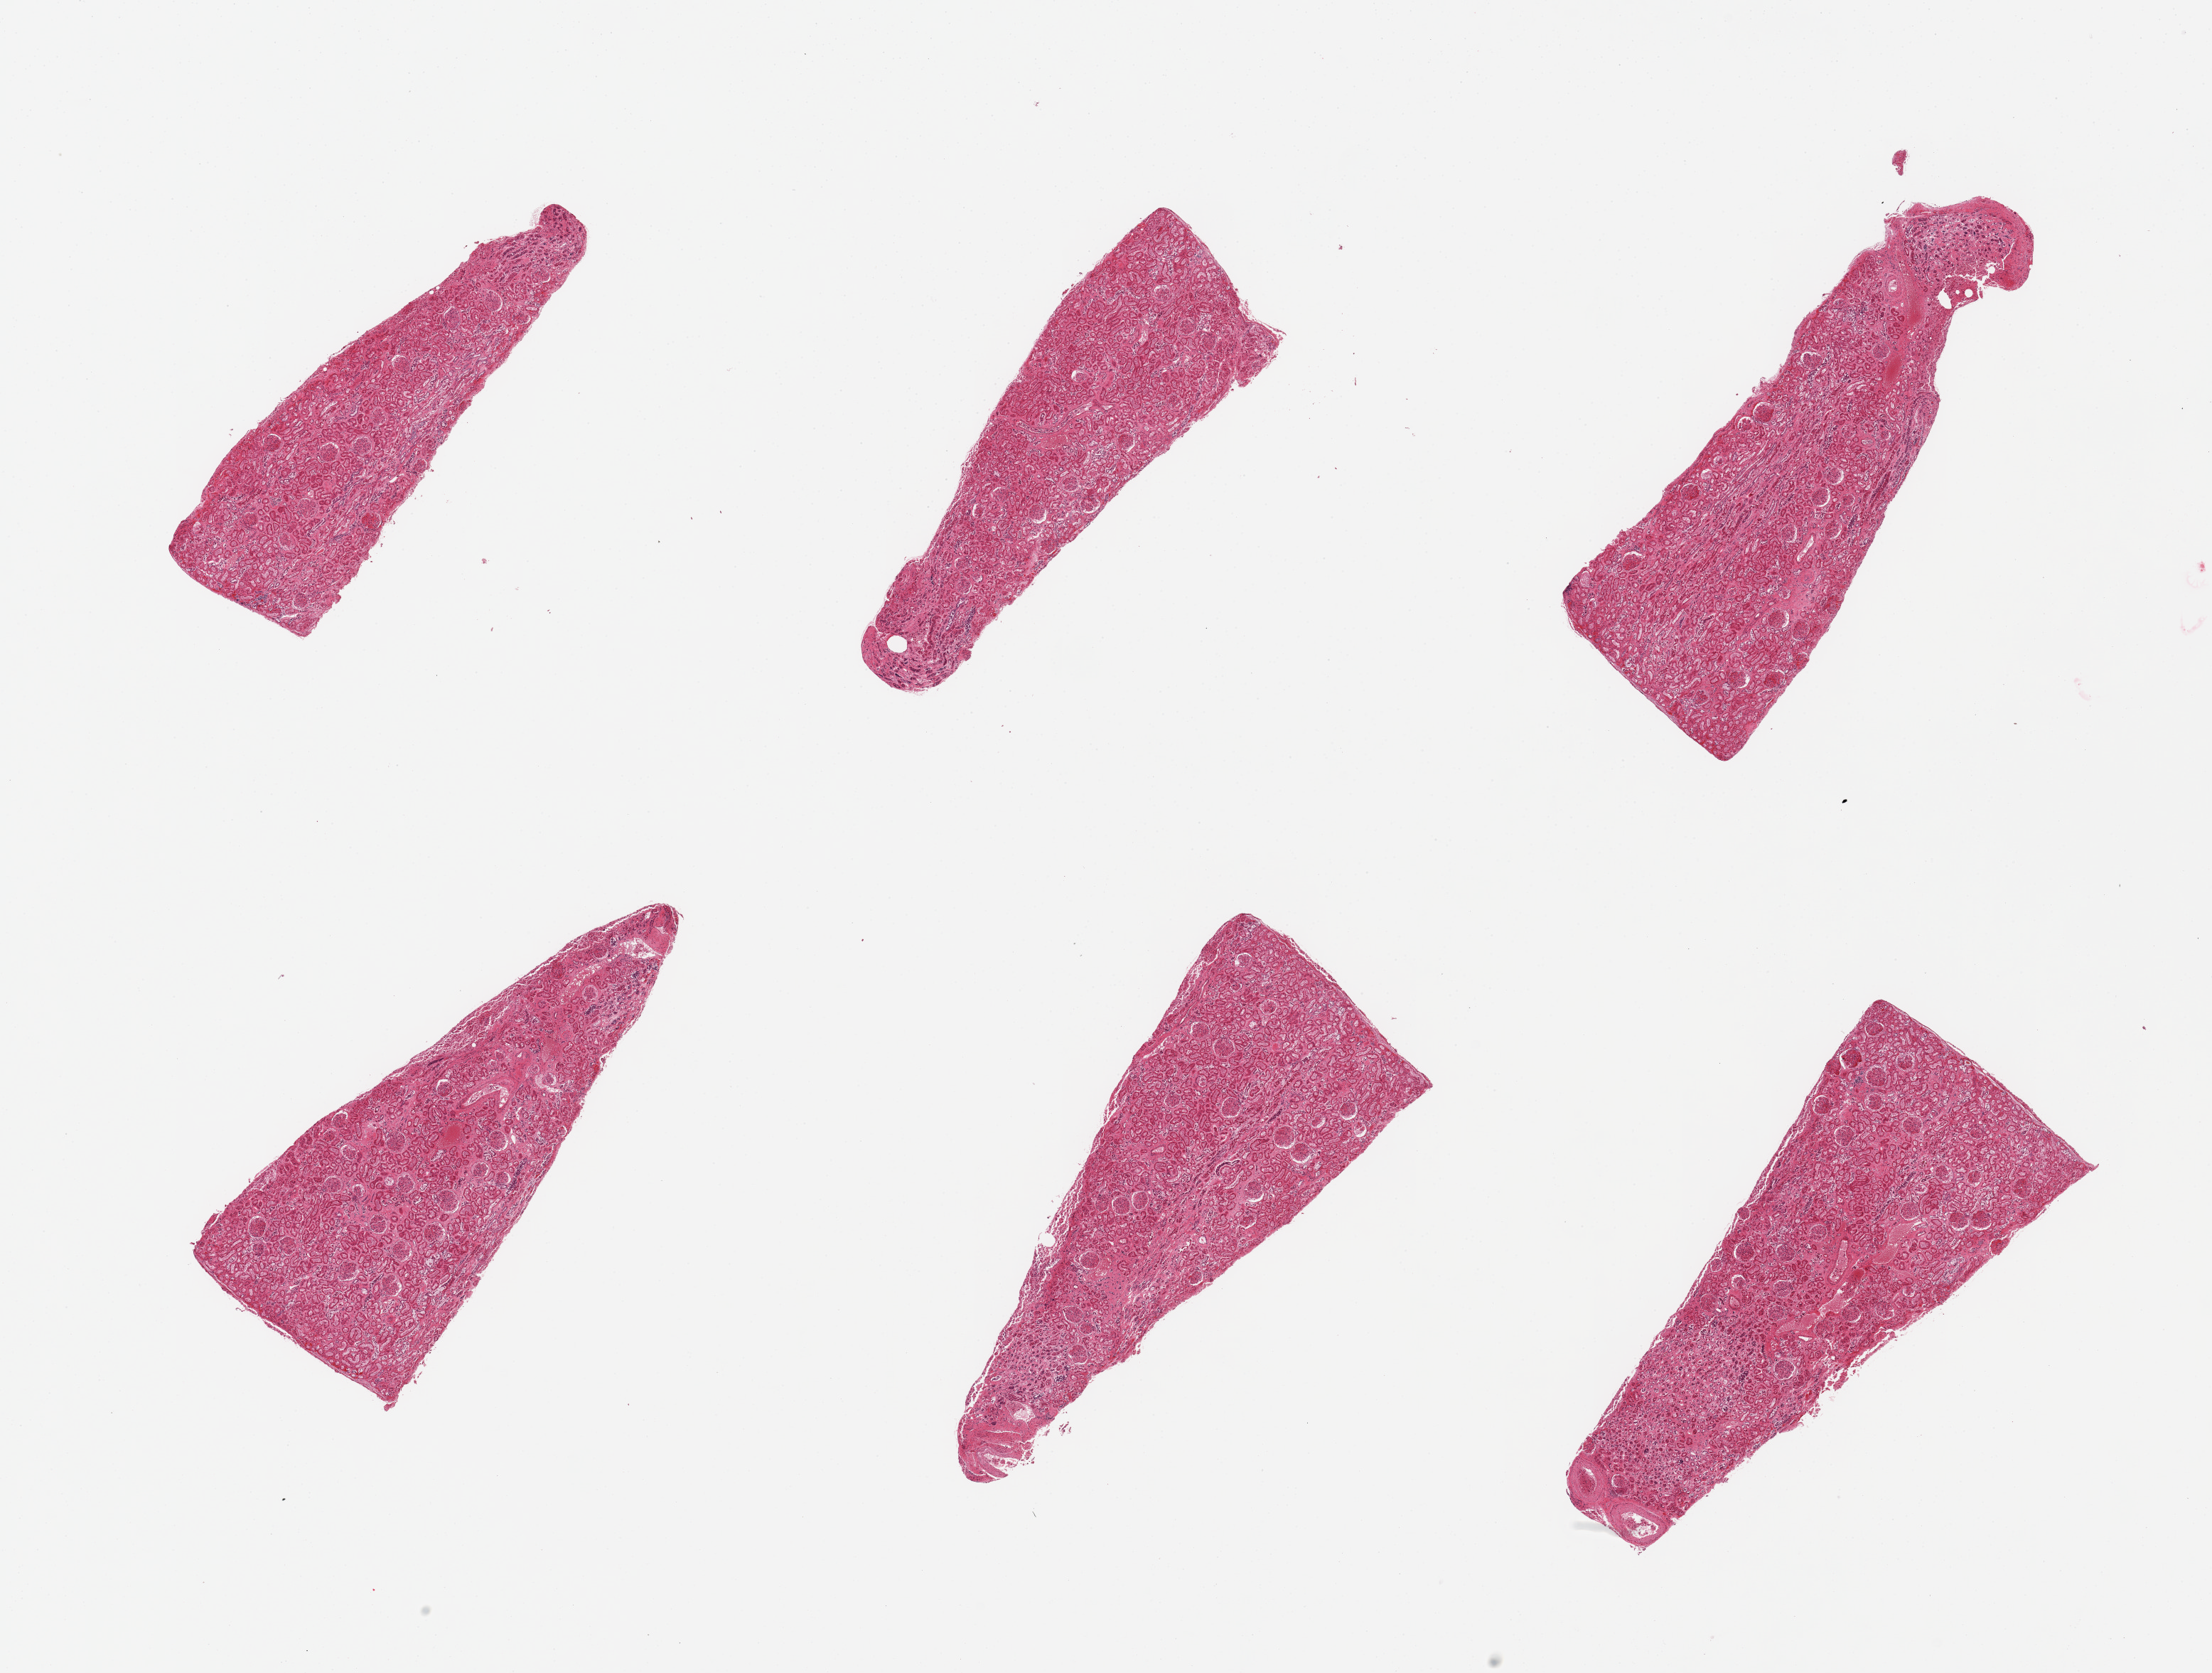
Whole-slide image, H&E stain, low-resolution overview of the scanned area, about 24.6 x 18.6 mm (slide scanned at 20x). PAXgene-fixed paraffin-embedded (PFPE) section. Section of renal cortex (target tissue). Tissue donor sample. Donor sex: male.
- review note (as recorded): 6 pieces; abundant glomeruli, no sclerosis (renal failure history)